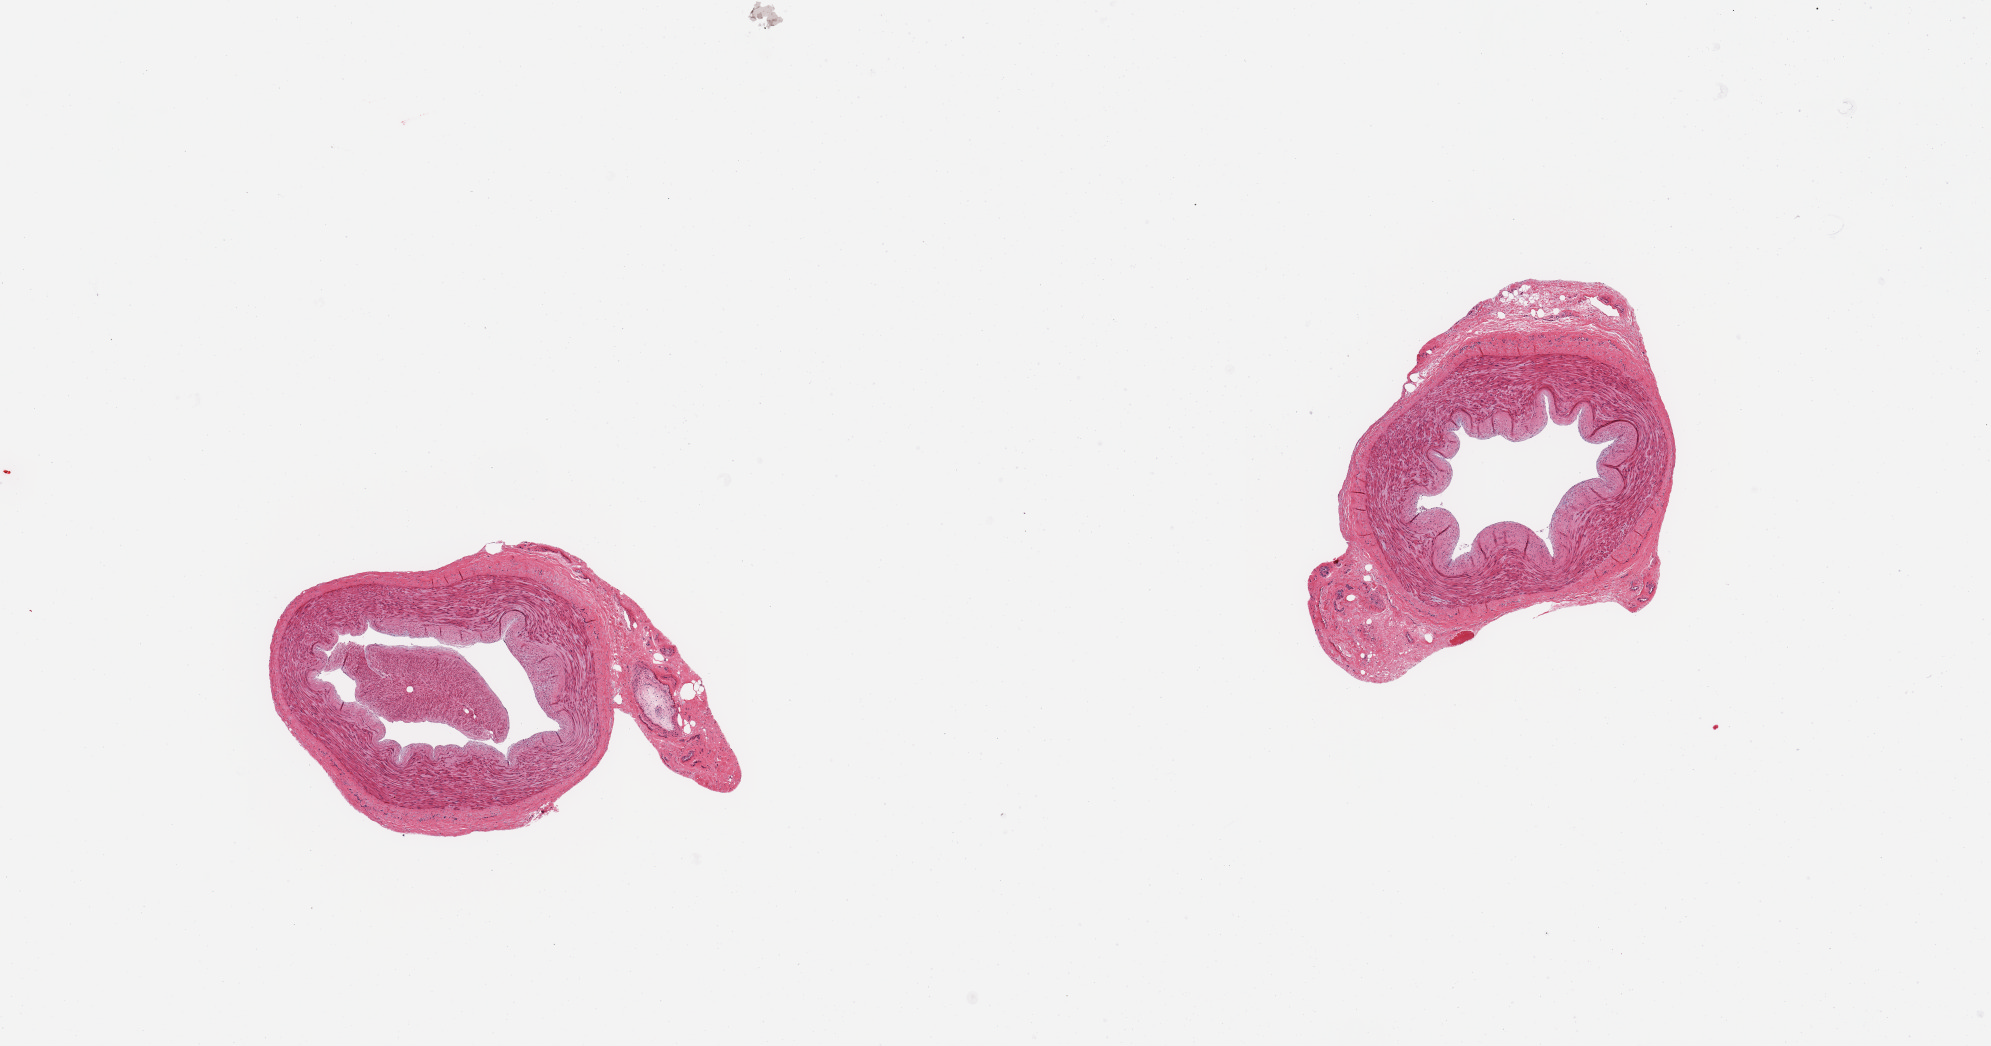
Whole-slide image, haematoxylin and eosin stain, brightfield, a low-resolution overview of the entire scanned area, about 15.8 x 8.3 mm (slide scanned at 20x), PAXgene-fixed paraffin-embedded (PFPE) section, section of tibial artery (target tissue), donor tissue sample. Donor: male.
Review note (as recorded): 2 pieces, nubbins of adherent fascia up to ~1mm.